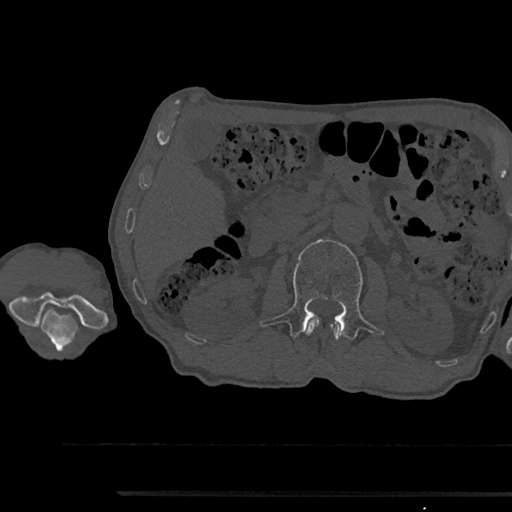
CT including the spine, one axial slice; slice 582 of 797 in the series (ordered by position); reconstruction kernel Br40s/3; 120 kVp; bone window (W 1800 / L 400 HU); 0.5 mm slice thickness; 512 × 512 image matrix. Male patient, age 79 years. From the clinical record (not read from this slice): primary cancer: prostate.
Outlined on this slice (semi-automatically segmented with operator editing):
- L1 vertebra: bounding box (x1, y1, x2, y2) in pixels: (307, 318, 343, 341)
- L2 vertebra: (259, 239, 383, 340)